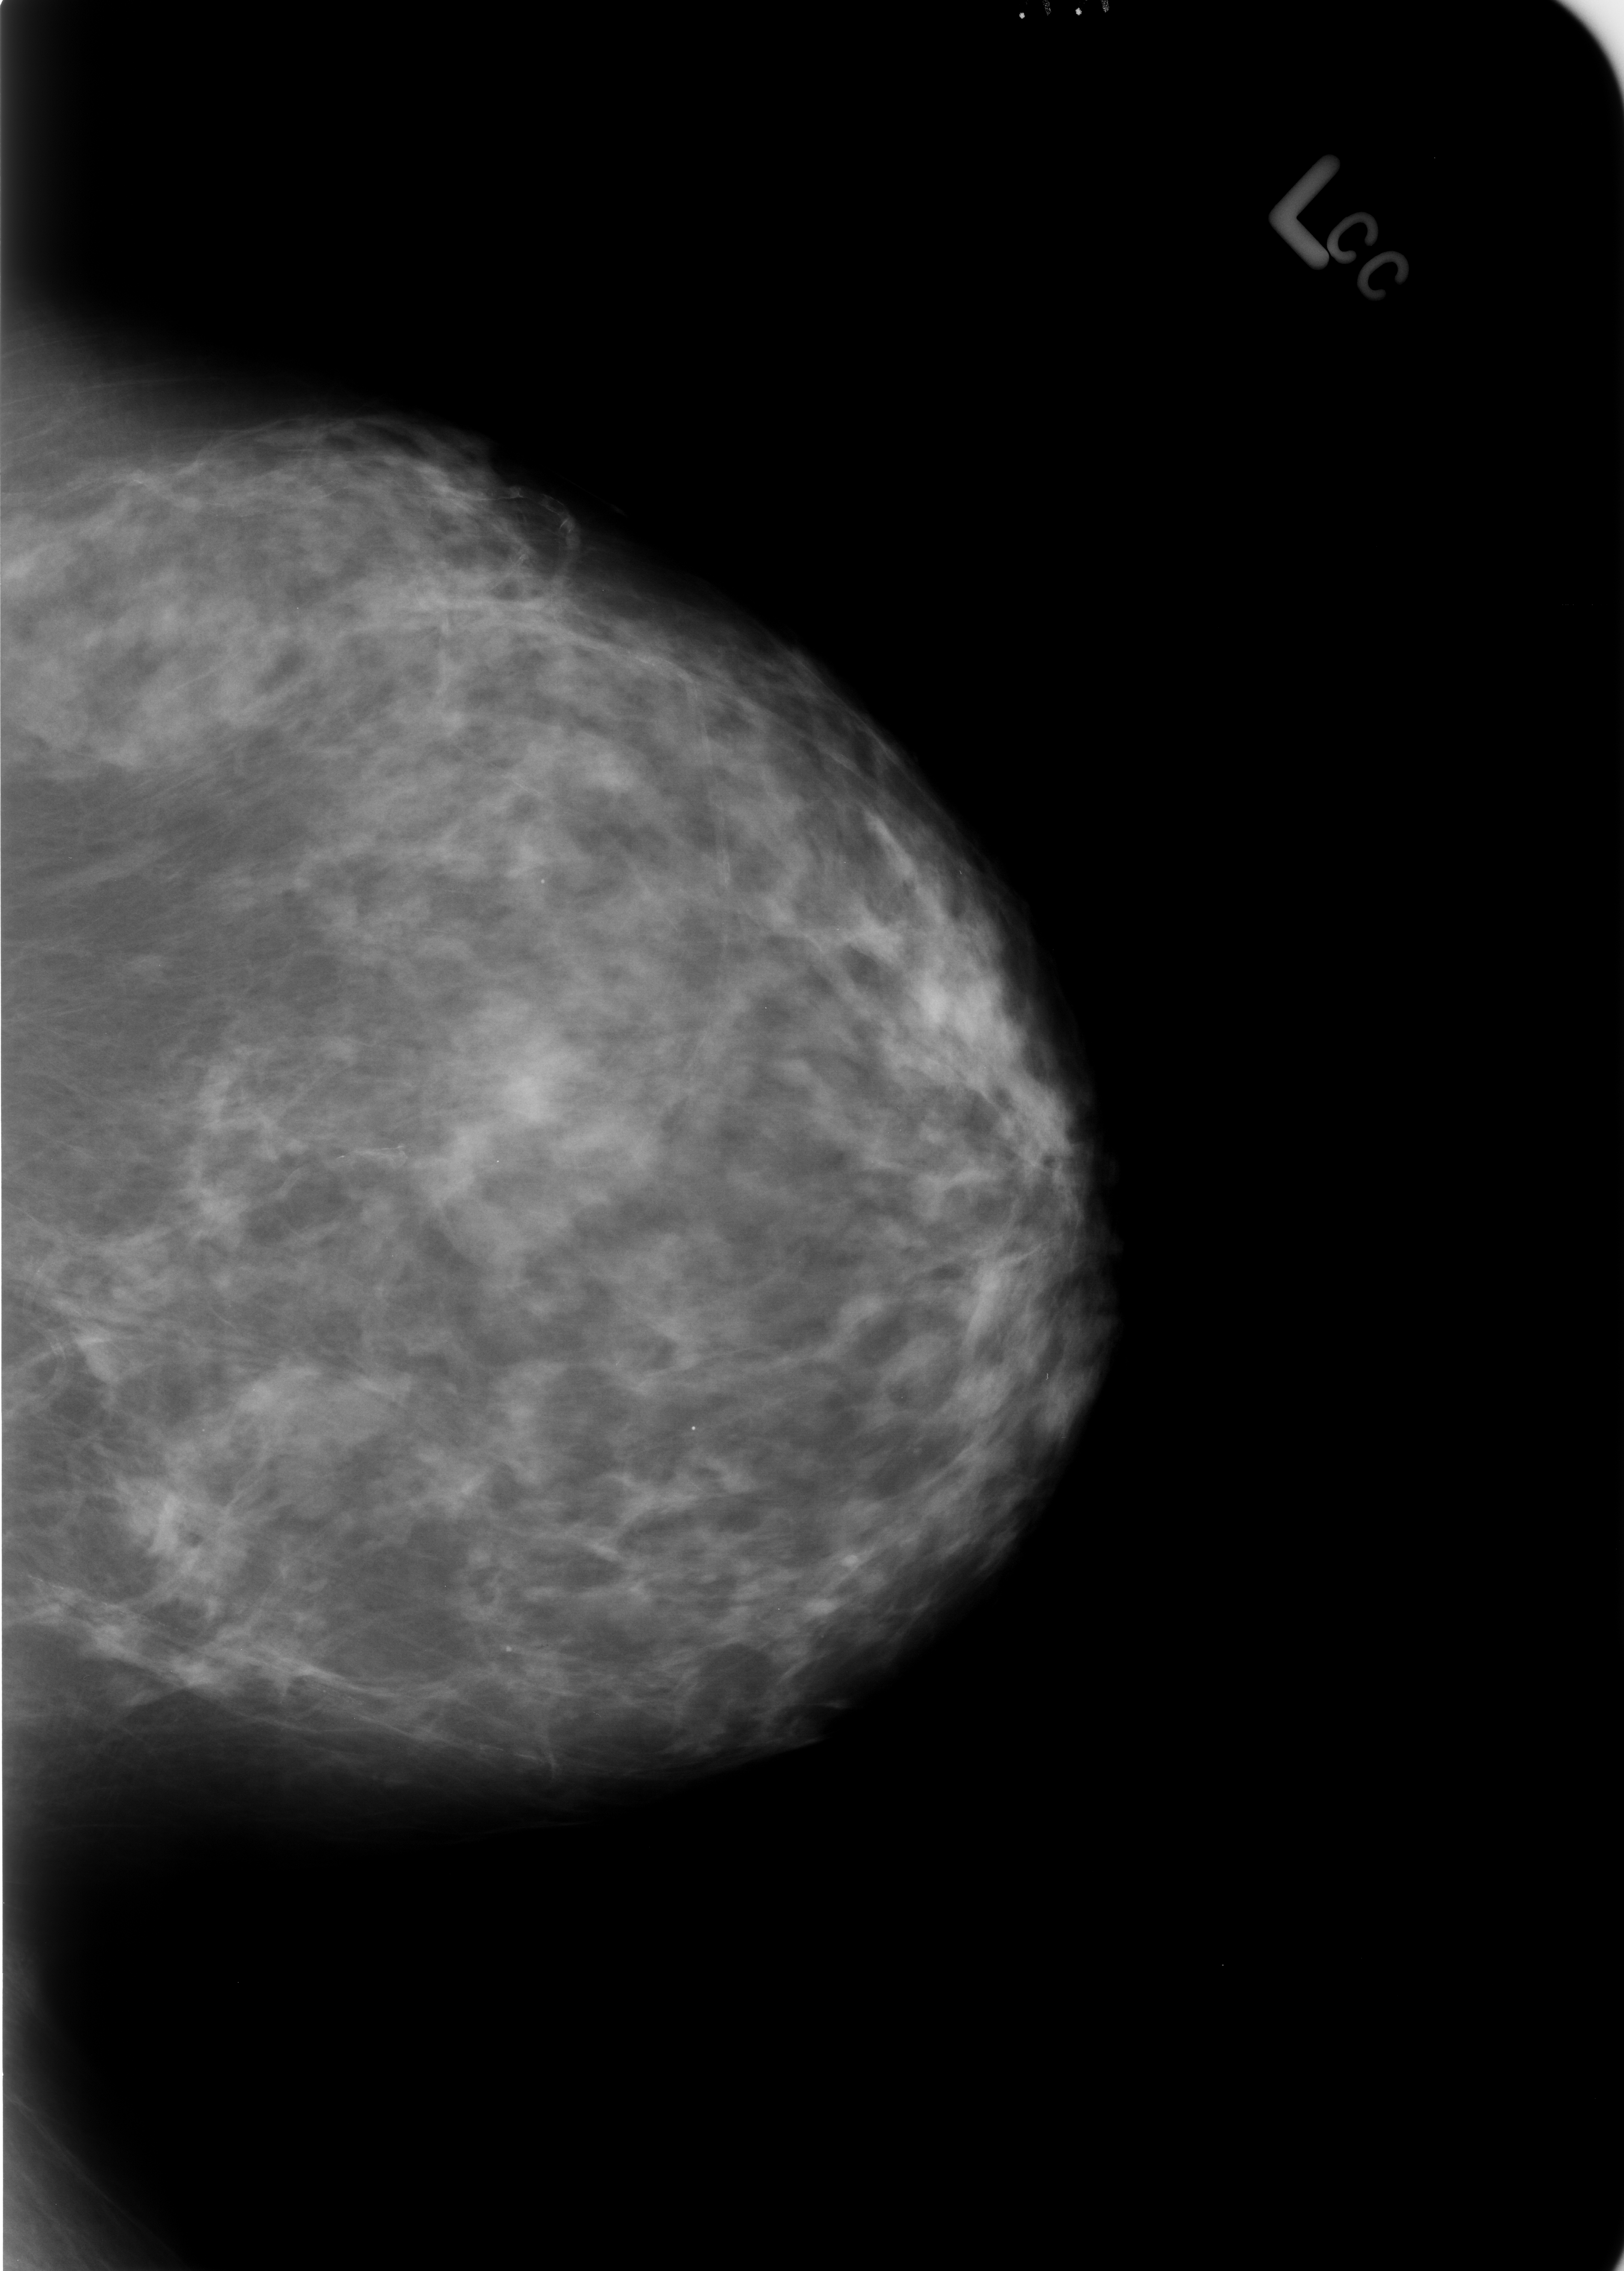
Scanned film-screen mammogram; left breast; CC view; BI-RADS breast density category 2 (scale 1–4).
Radiologist-marked abnormalities on this image: Finding 1 of 6: calcifications, morphology punctate; BI-RADS assessment category 2; benign; no additional work-up was recommended (benign without callback). Finding 2 of 6: calcifications, morphology punctate; BI-RADS assessment category 2; subtlety rating 4 on a 1 (subtle) to 5 (obvious) scale; benign; no additional work-up was recommended (benign without callback). Finding 3 of 6: calcifications, morphology vascular; BI-RADS assessment category 2; subtlety rating 4 on a 1 (subtle) to 5 (obvious) scale; benign without callback (not worked up further). Finding 4 of 6: calcifications, morphology vascular; BI-RADS assessment category 2; benign without callback (not worked up further). Finding 5 of 6: calcifications, morphology vascular; BI-RADS assessment category 2; subtlety rating 4 on a 1 (subtle) to 5 (obvious) scale; benign without callback (not worked up further). Finding 6 of 6: calcifications, morphology vascular; BI-RADS assessment category 2; benign without callback (not worked up further).